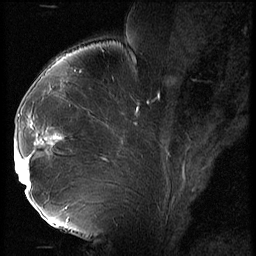
Breast MRI (dynamic contrast-enhanced), one sagittal slice. Position 36 of 56 along the scan axis. 3 images stored at this slice position (order not interpretable as contrast timing). 1.5 T. TE 4.2 ms, TR 9 ms. 256 × 256 image matrix, field of view 180 × 180 mm. Female patient, age 43 years. Case-level facts recorded for this patient, not image findings: setting: breast cancer imaged before/during neoadjuvant chemotherapy; receptor status: HER2-positive.
Structures marked on this image (semi-automatically segmented with operator editing):
- analysis volume of interest (the breast-tissue region the enhancement analysis was run in; not a lesion): bounding box <15,92,74,211> (left, top, right, bottom; pixels)
- tumour enhancement mask (voxels above the 140 % enhancement threshold inside the analysis volume of interest): <15,136,62,195>